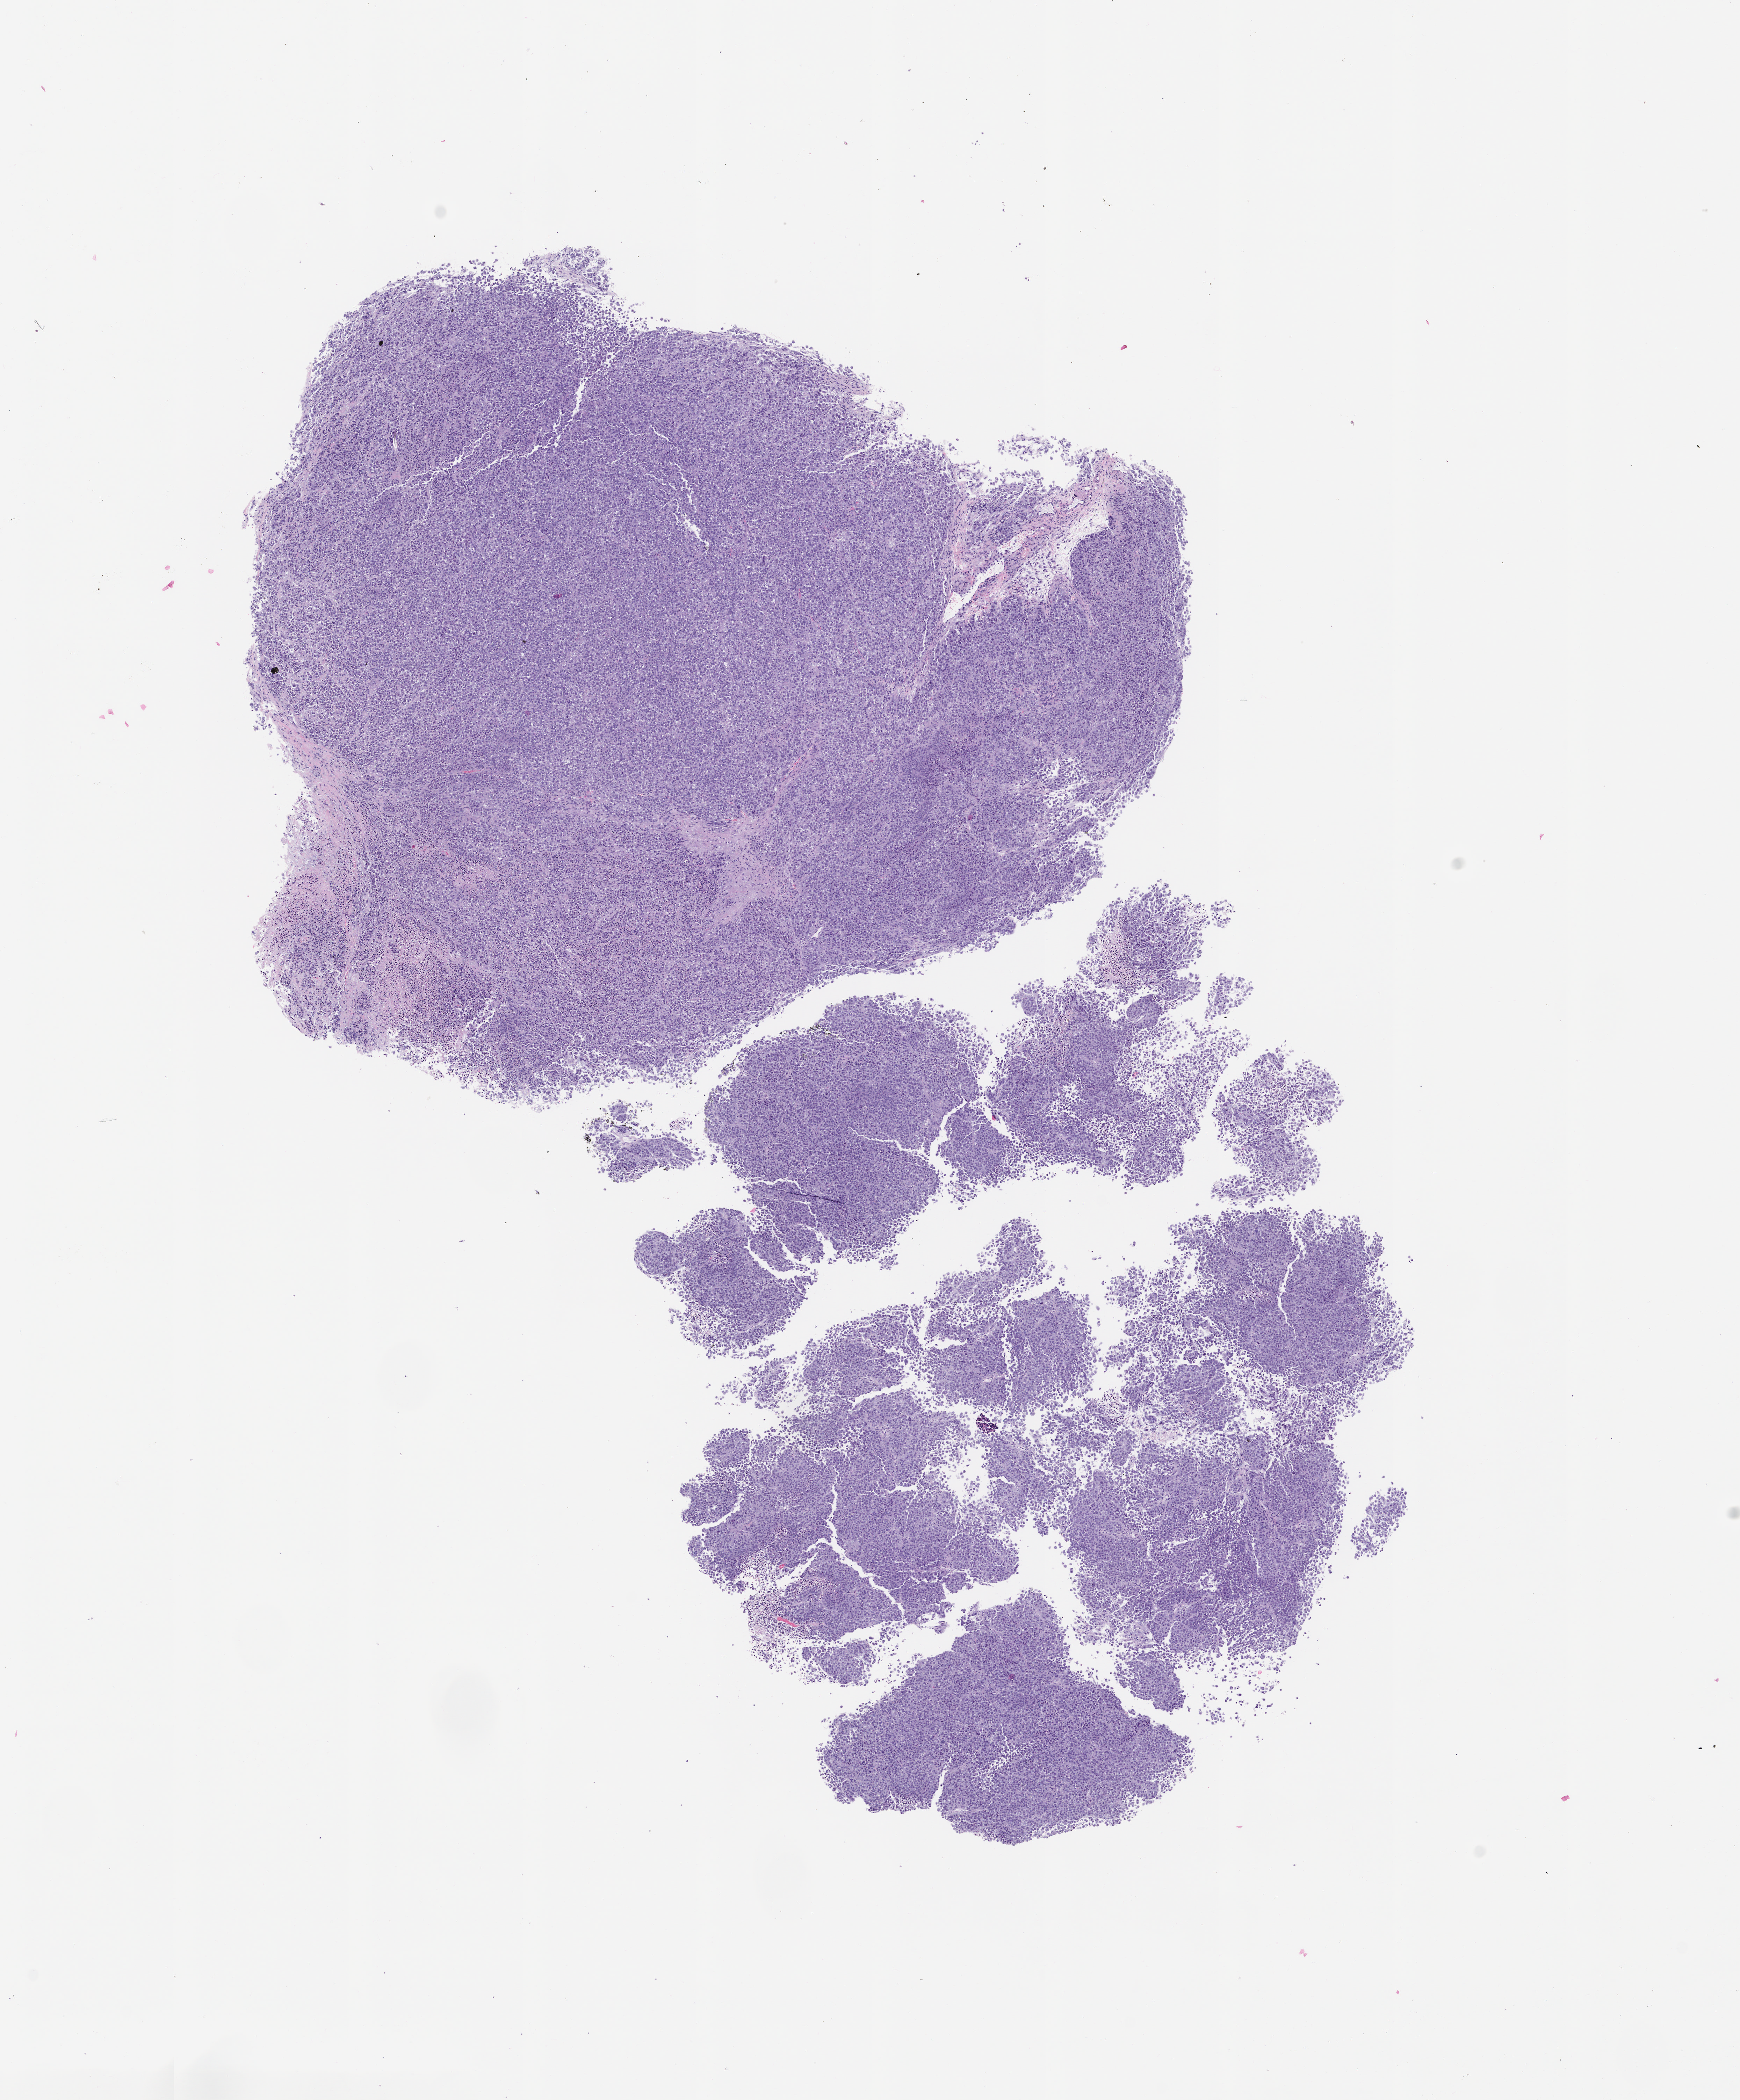
Whole-slide image, haematoxylin and eosin: patient-derived xenograft (human tumor grown in a mouse), passage 3 — whole scanned area (about 10.0 x 12.0 mm) shown as a low-resolution overview, formalin-fixed paraffin-embedded section, tumor site category: skin.
* originating patient diagnosis: Melanoma